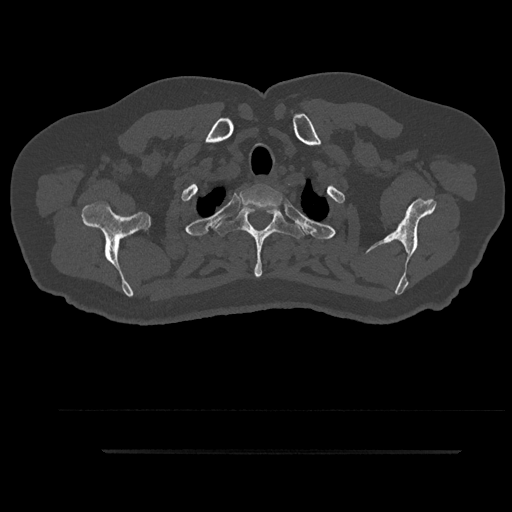
CT including the spine, one axial slice; position 769 of 797 along the scan axis; reconstruction kernel Br40s/3; 120 kVp; bone window (W 1800 / L 400 HU); 512 × 512 image matrix, field of view 432 × 432 mm. Male patient, age 63 years. From the clinical record (not read from this slice): primary cancer: renal; vertebrae with lytic lesions (as recorded): T8.
Annotated regions visible in this slice (semi-automatically segmented with operator editing):
- T1 vertebra: box from (x=239, y=185) to (x=282, y=231) px
- T2 vertebra: (x=214, y=206)–(x=305, y=278)